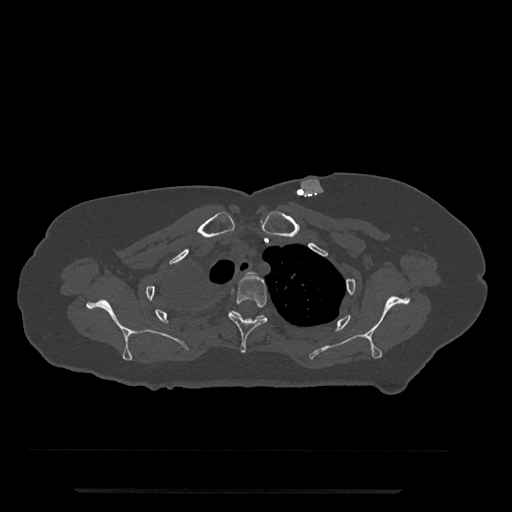
CT including the spine, one axial slice. Slice 627 of 797 in the series (ordered by position). Reconstruction kernel Br40s/3. 120 kVp. Bone window (W 1800 / L 400 HU). 0.5 mm slice thickness. 512 × 512 image matrix, field of view 440 × 440 mm. Female patient, age 51 years. From the clinical record (not read from this slice): primary cancer: neuro; vertebrae with lytic lesions (as recorded): T8.
Annotated regions visible in this slice (semi-automatically segmented with operator editing):
- T3 vertebra: box from (x=228, y=273) to (x=268, y=353) px
- T4 vertebra: (x=231, y=311)–(x=265, y=319)